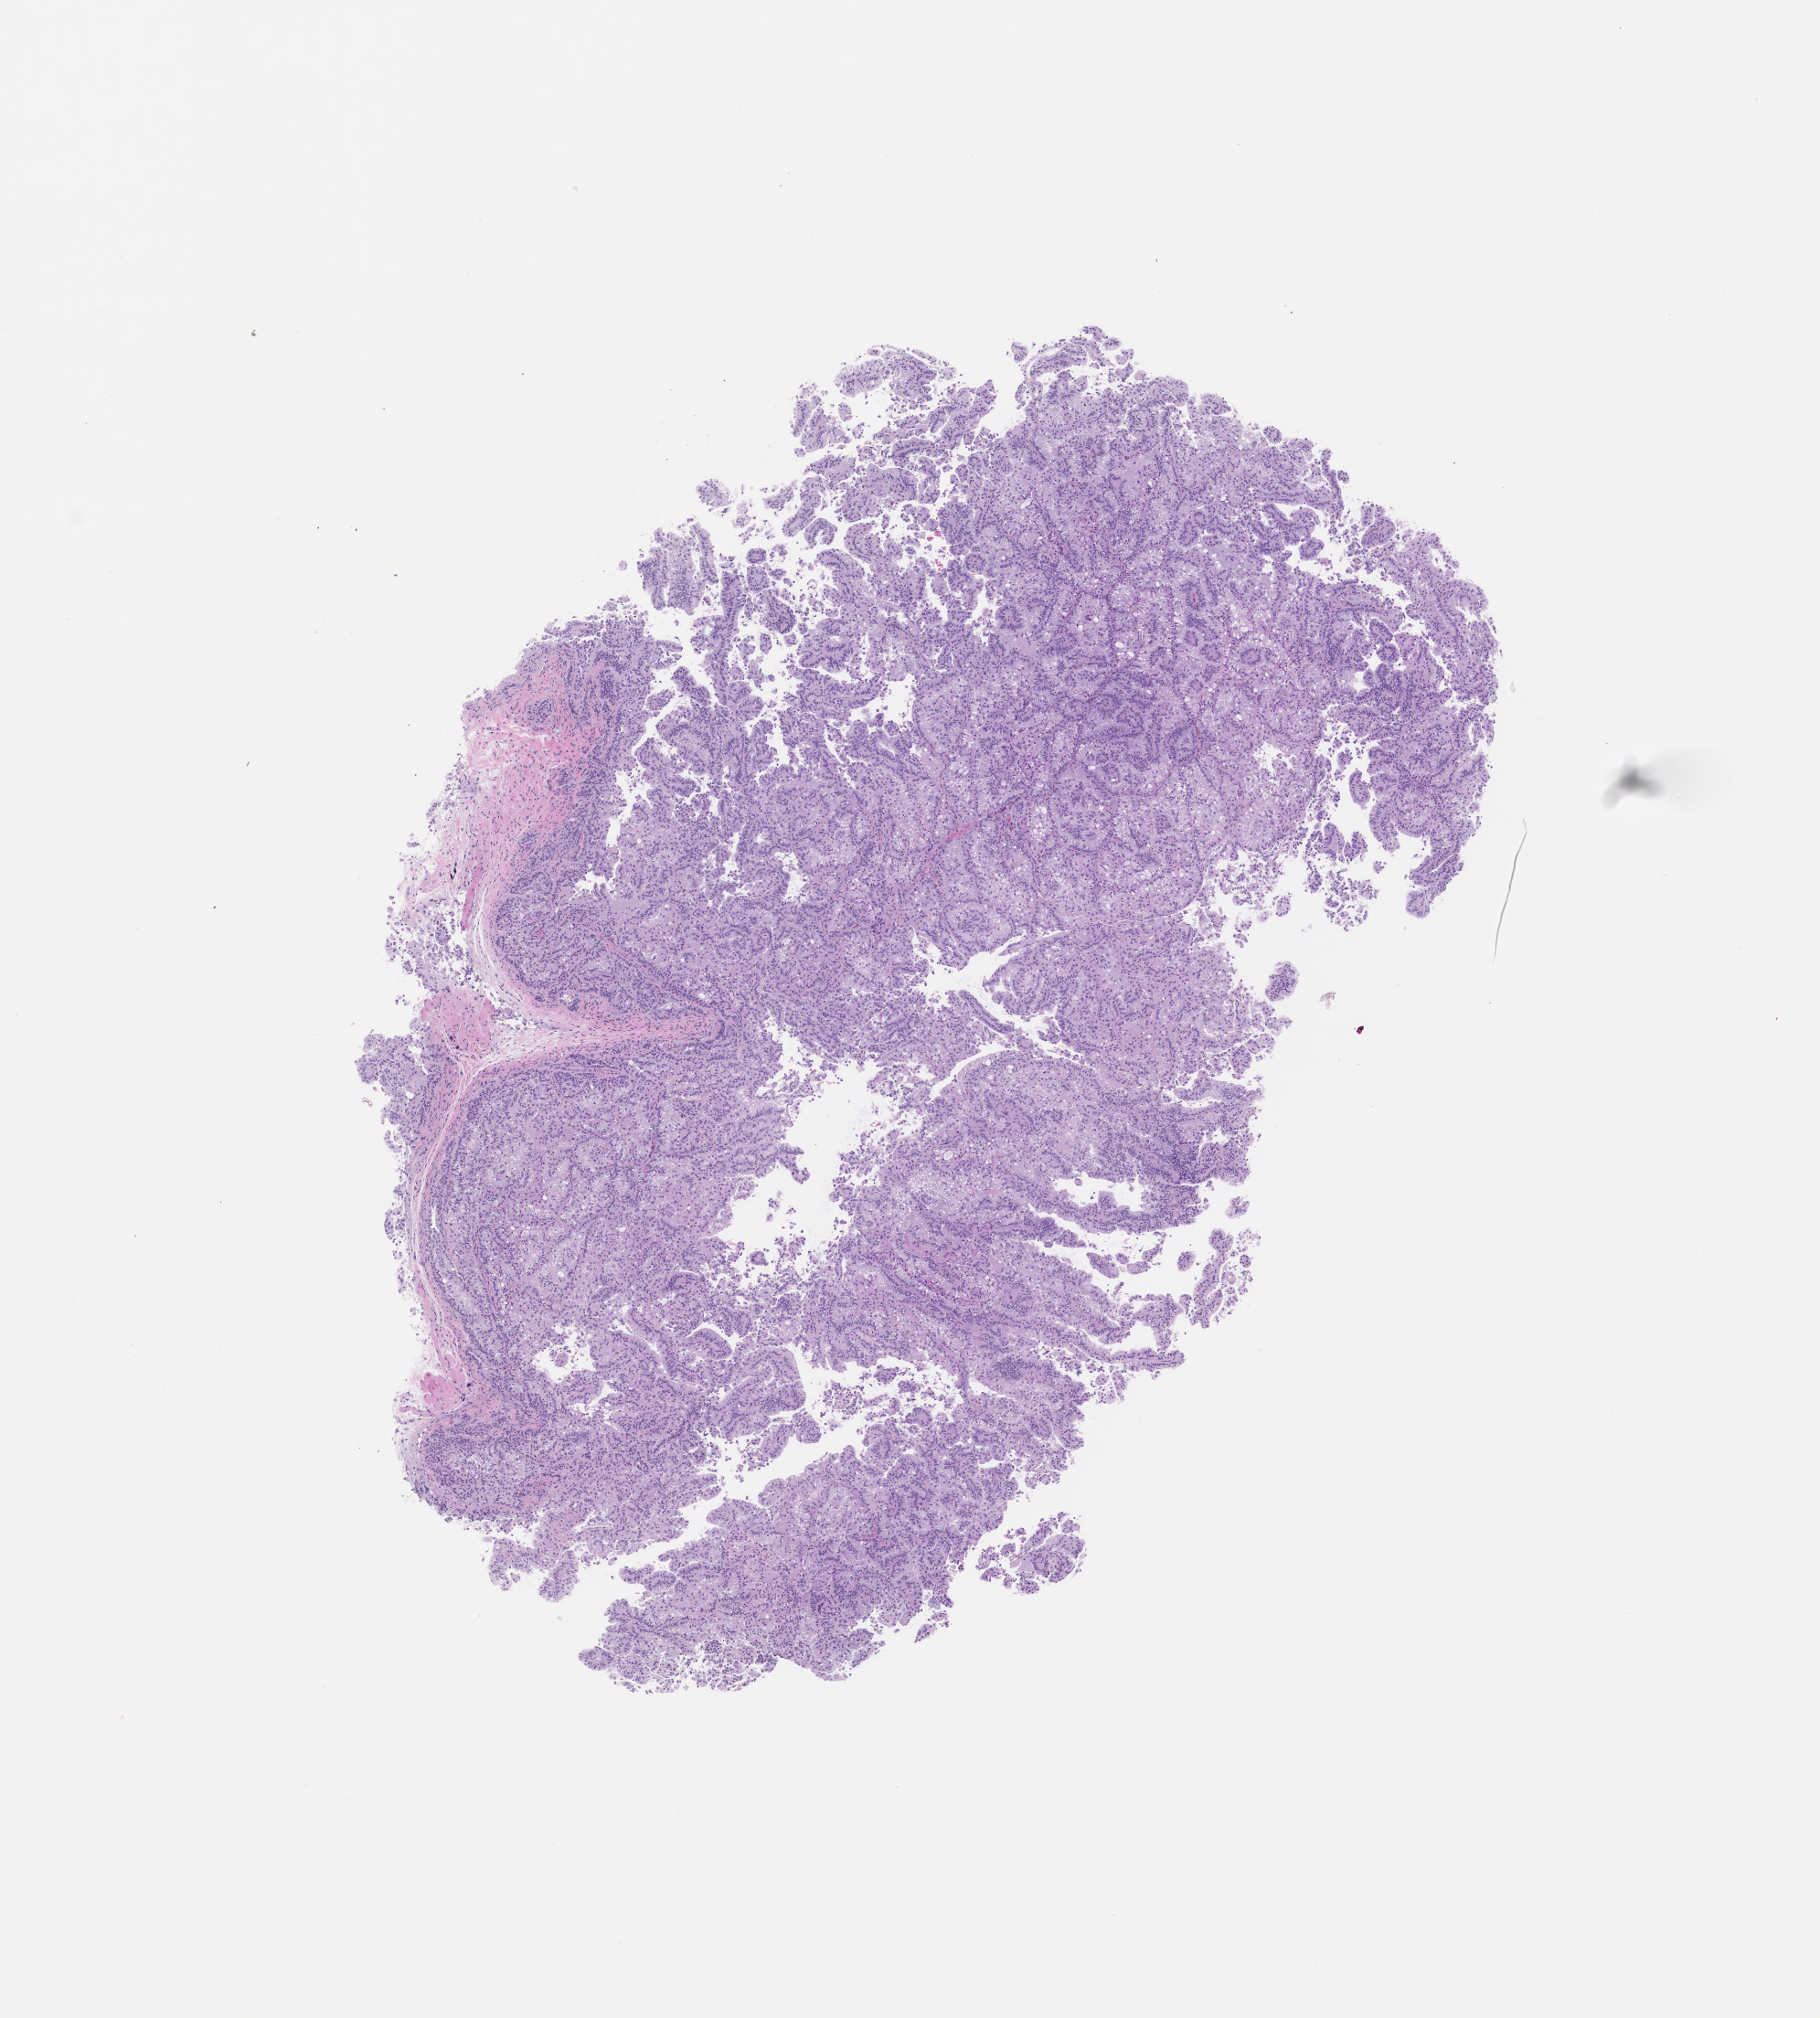
Whole-slide image, hematoxylin and eosin (H&E): patient-derived xenograft (human tumor grown in a mouse), passage 2, low-resolution overview of the scanned area, about 8.0 x 8.8 mm, formalin-fixed, paraffin-embedded (FFPE) tissue, tumor site category: genitourinary tract.
Originating patient diagnosis: Renal Cell Carcinoma, Not Otherwise Specified.